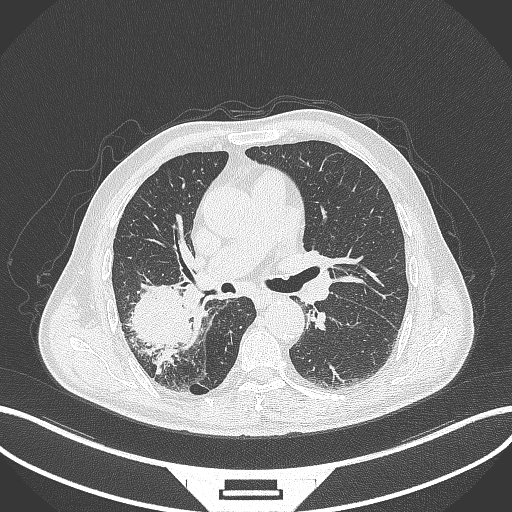
Chest CT, one axial slice; position 236 of 429 along the scan axis; 120 kVp; lung window (W 1500 / L -600 HU); 1 mm slice thickness; 512 × 512 image matrix, field of view 400 × 400 mm. Male patient, age 72 years. Case-level facts recorded for this patient, not image findings: clinical TNM (as recorded): T3 N2 M0.
Outlined on this slice (bounding box drawn by a radiologist):
- lung tumour (recorded histology: adenocarcinoma): box from (x=126, y=277) to (x=193, y=351) px